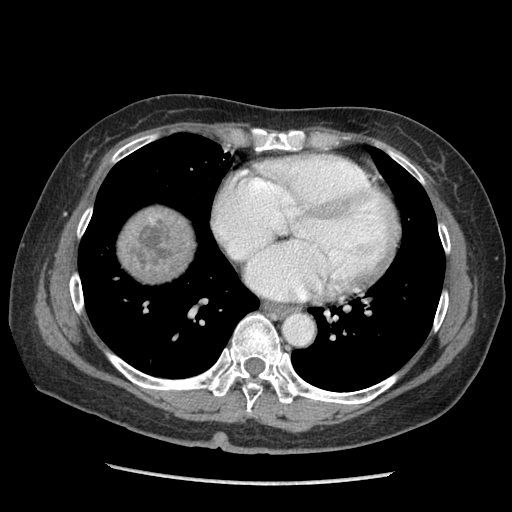
Contrast-enhanced abdominal CT (liver protocol), one axial slice. Position 97 of 105 along the scan axis. Reconstruction kernel STANDARD. Soft-tissue window (W 400 / L 40 HU). 2.5 mm slice thickness. 512 × 512 image matrix, field of view 340 × 340 mm. Case-level facts recorded for this patient, not image findings: diagnosis: hepatocellular carcinoma (patient treated with transarterial chemoembolisation; whether this scan precedes or follows treatment is not stated here); TNM stage (as recorded): Stage-I; Child-Pugh class: A; tumour differentiation: moderately differentiated; tumour size: 11.1 cm.
Annotated regions visible in this slice (semi-automatic segmentation, software-assisted and operator-edited):
- liver parenchyma outside the tumour (the mass and vessels are separate outlines, so this box may not span the whole liver): bounding box (x1, y1, x2, y2) in pixels: (120, 206, 192, 280)
- mass: (128, 217, 177, 272)